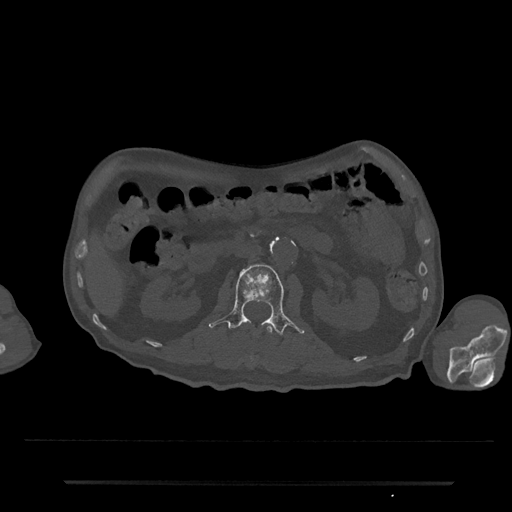
CT including the spine, one axial slice. Position 76 of 797 along the scan axis. Reconstruction kernel Br40s/3. Bone window (W 1800 / L 400 HU). 0.5 mm slice thickness. 512 × 512 image matrix, field of view 427 × 427 mm. Patient: male, 74 years. From the clinical record (not read from this slice): primary cancer: prostate.
Outlined on this slice (semi-automatically segmented with operator editing):
- L1 vertebra: bounding box [x1, y1, x2, y2] px = [249, 325, 273, 365]
- L2 vertebra: [209, 264, 304, 337]